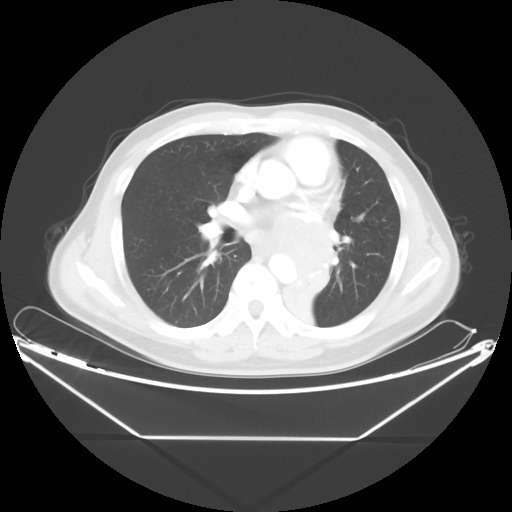
Chest CT, one axial slice; slice 24 of 48 in the series (ordered by position); reconstruction kernel STANDARD; 120 kVp; lung window (W 1500 / L -600 HU); 512 × 512 image matrix, field of view 438 × 438 mm. Patient: male, 58 years. Case-level facts recorded for this patient, not image findings: clinical TNM (as recorded): T3 N3 M0.
Structures marked on this image (bounding box drawn by a radiologist):
- lung tumour (recorded histology: squamous cell carcinoma): bounding box [x1, y1, x2, y2] px = [278, 243, 368, 330]